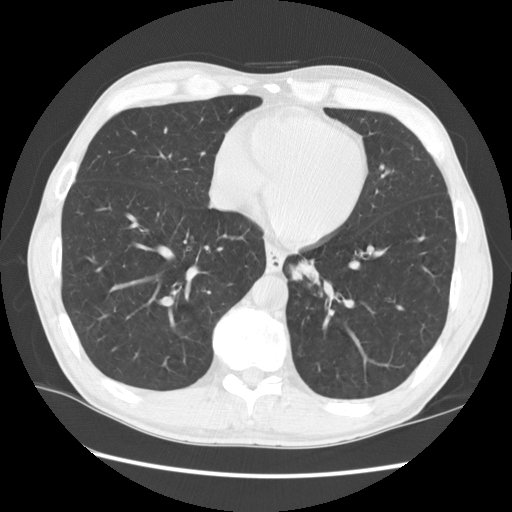
Low-dose screening chest CT, axial slice, first (baseline) screen, lung window (W 1500 / L -600 HU), 2.5 mm slice thickness, slice 98 of 141 in the series. Male participant, aged 57 years at enrolment. Current smoker at enrolment.
Expert reader's lesion annotation, box from (x=268, y=244) to (x=340, y=307) px. The screening reader recorded 2 non-calcified nodules or masses ≥4 mm on this exam; which of them this box marks is not recorded. Participant outcome: lung cancer diagnosed 95 days after this screen — squamous cell carcinoma, NOS, left lower lobe, moderately differentiated (G2), stage IB (AJCC 6th edition), 35 mm at pathology.